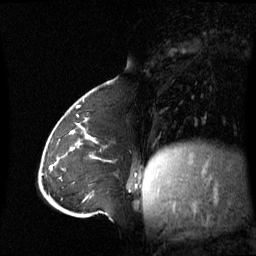
Breast MRI (dynamic contrast-enhanced), one sagittal slice; position 22 of 60 along the scan axis; dynamic contrast-enhanced series, image 2 of 3 at this slice position (ordered by acquisition); 1.5 T; TE 4.2 ms, TR 8.4 ms; 2.8 mm slice thickness; 256 × 256 image matrix, field of view 270 × 270 mm. Female patient, age 43 years. Case-level facts recorded for this patient, not image findings: setting: breast cancer imaged before/during neoadjuvant chemotherapy; receptor status: triple-negative.
Structures marked on this image (semi-automatically segmented with operator editing):
- analysis volume of interest (the breast-tissue region the enhancement analysis was run in; not a lesion): bounding box (x1, y1, x2, y2) in pixels: (62, 124, 137, 180)
- tumour enhancement mask (voxels above the 70 % enhancement threshold inside the analysis volume of interest): (70, 130, 136, 176)